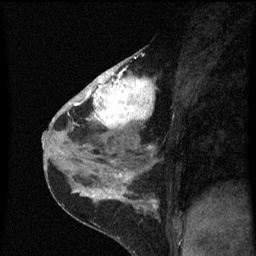
Breast MRI (dynamic contrast-enhanced), one sagittal slice. Slice 34 of 60 in the series (ordered by position). Dynamic contrast-enhanced series, image 2 of 3 at this slice position (ordered by acquisition). 1.5 T. TE 4.2 ms, TR 8 ms. 2 mm slice thickness. 256 × 256 image matrix, field of view 180 × 180 mm. Patient: female, 38 years.
Structures marked on this image (semi-automatic segmentation, software-assisted and operator-edited):
- analysis volume of interest (the breast-tissue region the enhancement analysis was run in; not a lesion): bounding box <80,52,157,151> (left, top, right, bottom; pixels)
- tumour enhancement mask (voxels above the 70 % enhancement threshold inside the analysis volume of interest): <80,68,157,147>